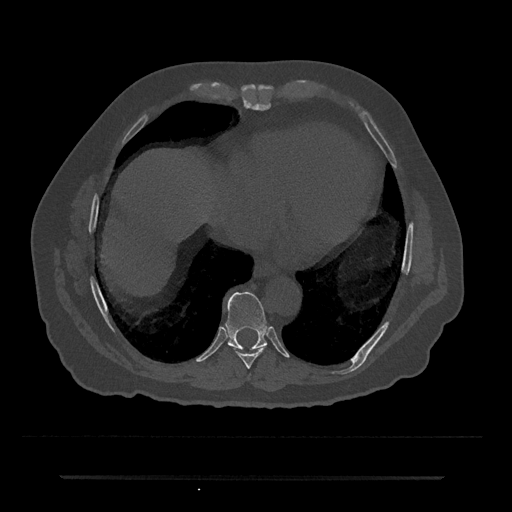
CT including the spine, one axial slice; position 304 of 797 along the scan axis; reconstruction kernel Br40s/3; bone window (W 1800 / L 400 HU); 0.5 mm slice thickness; 512 × 512 image matrix. Patient: male, 69 years. From the clinical record (not read from this slice): primary cancer: prostate.
Outlined on this slice (semi-automatically segmented with operator editing):
- T8 vertebra: bounding box <235,346,266,368> (left, top, right, bottom; pixels)
- T9 vertebra: <226,291,267,350>